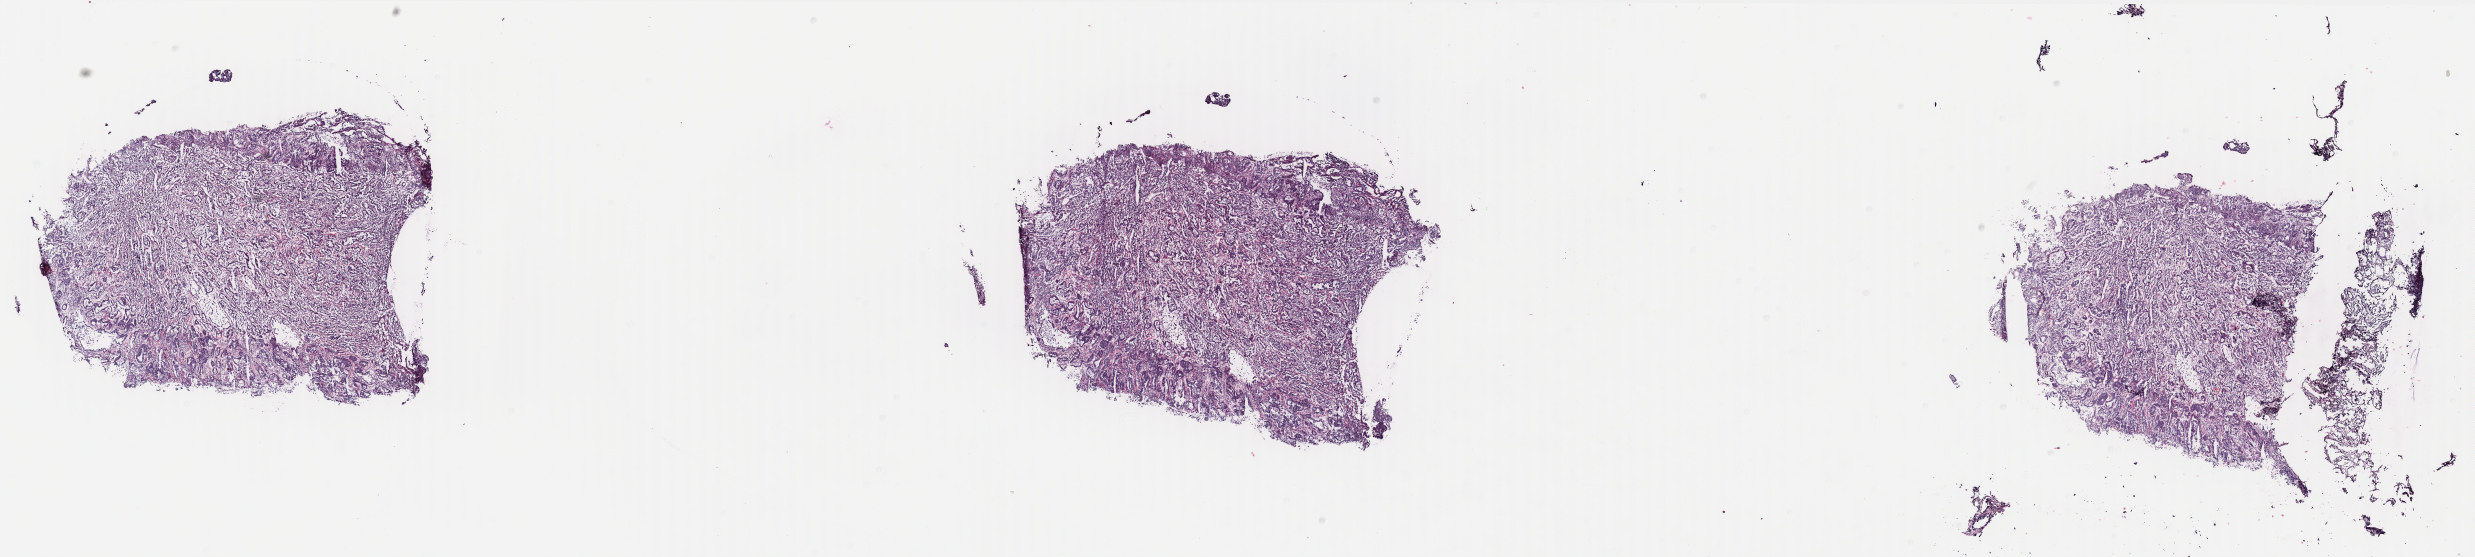
Whole-slide histology image, Hematoxylin and eosin (H&E) stained — a low-resolution overview of the entire scanned area, about 39.7 x 8.9 mm (slide scanned at 40x), frozen section from the top of the tissue portion, primary tumour sample from the uterus. Female patient; age at initial diagnosis 69 years.
Diagnosis: Endometrioid adenocarcinoma, NOS (endometrium).